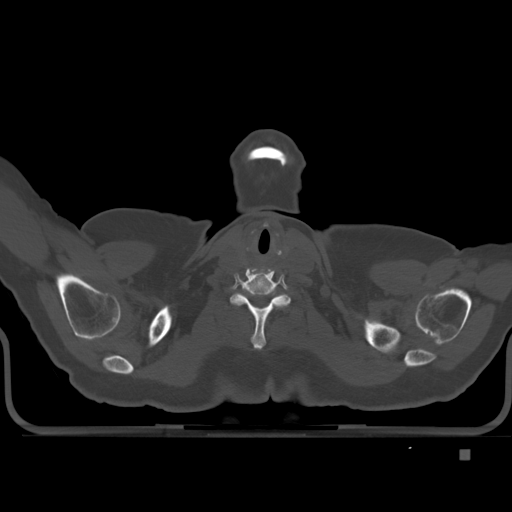
CT including the spine, one axial slice; slice 415 of 477 in the series (ordered by position); bone window (W 1800 / L 400 HU); 1.5 mm slice thickness; 512 × 512 image matrix. Female patient, age 74 years. From the clinical record (not read from this slice): primary cancer: colon.
Structures marked on this image (semi-automatic segmentation, software-assisted and operator-edited):
- T1 vertebra: bounding box <267,311,271,318> (left, top, right, bottom; pixels)